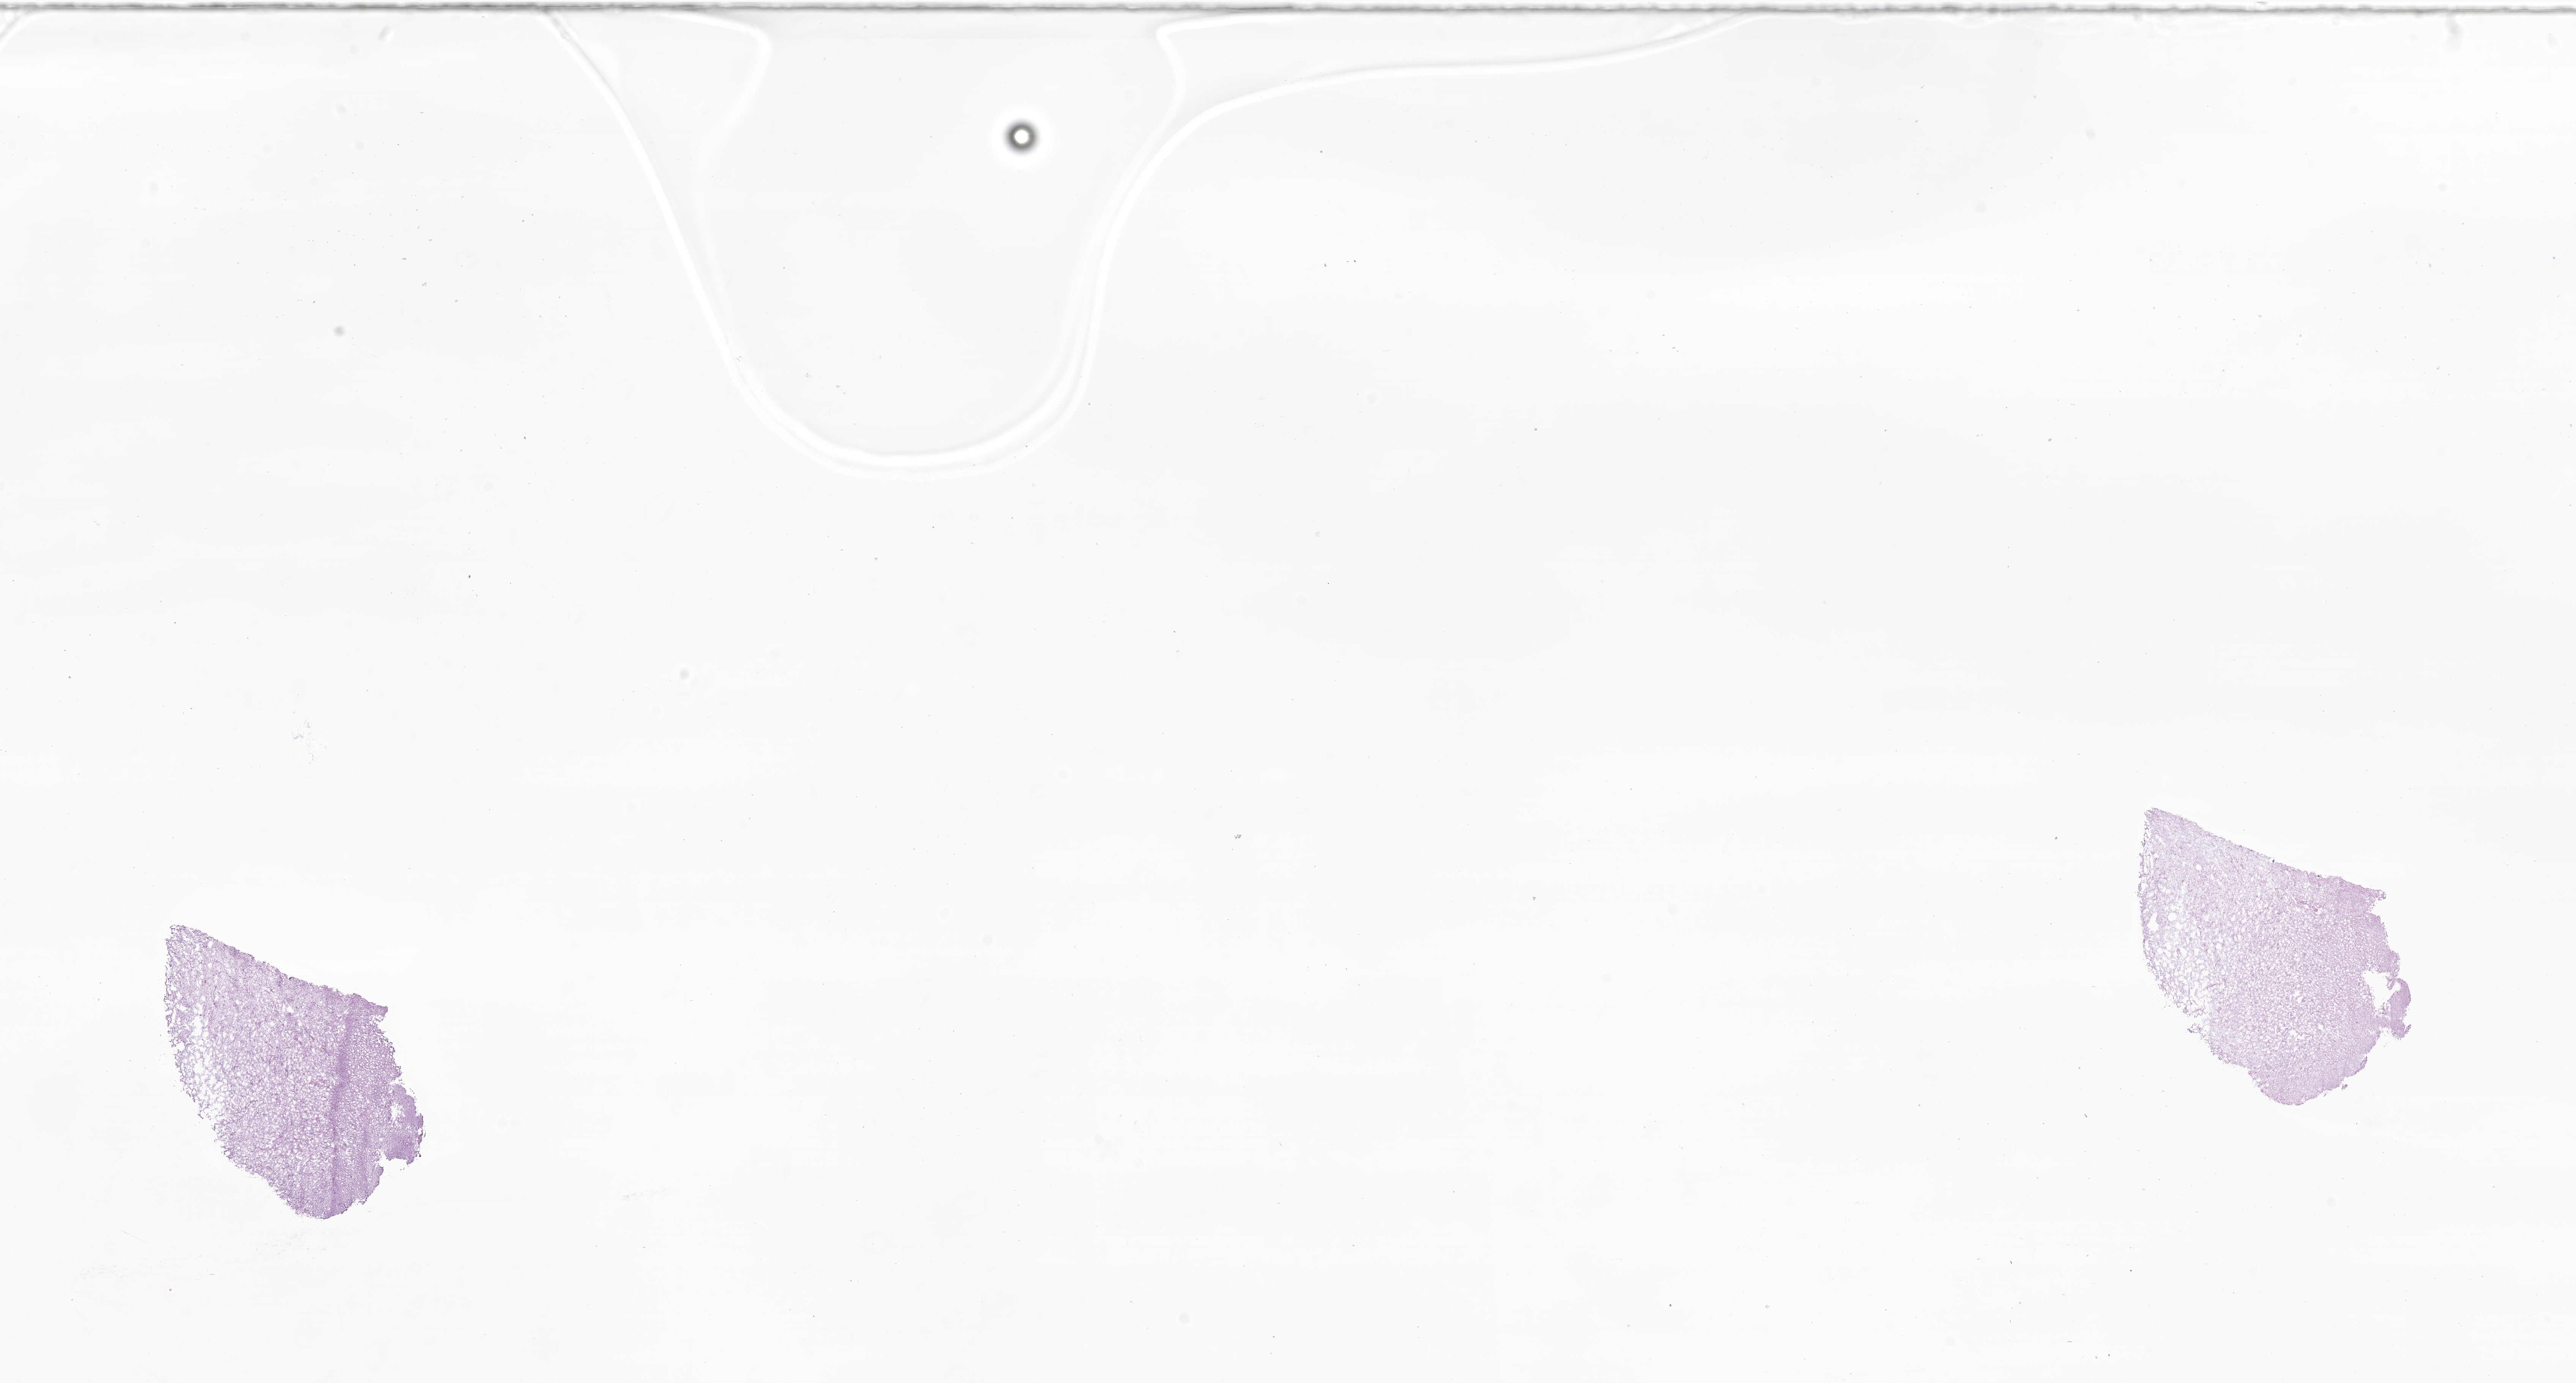
Digitized haematoxylin and eosin-stained section of tumor tissue from the frontal lobe — low-resolution overview of the scanned area, about 28.6 x 15.4 mm; cryosection (OCT / tissue freezing medium). Female patient, age 71 months (5 years 11 months).
Recorded diagnosis: Astrocytoma, NOS.